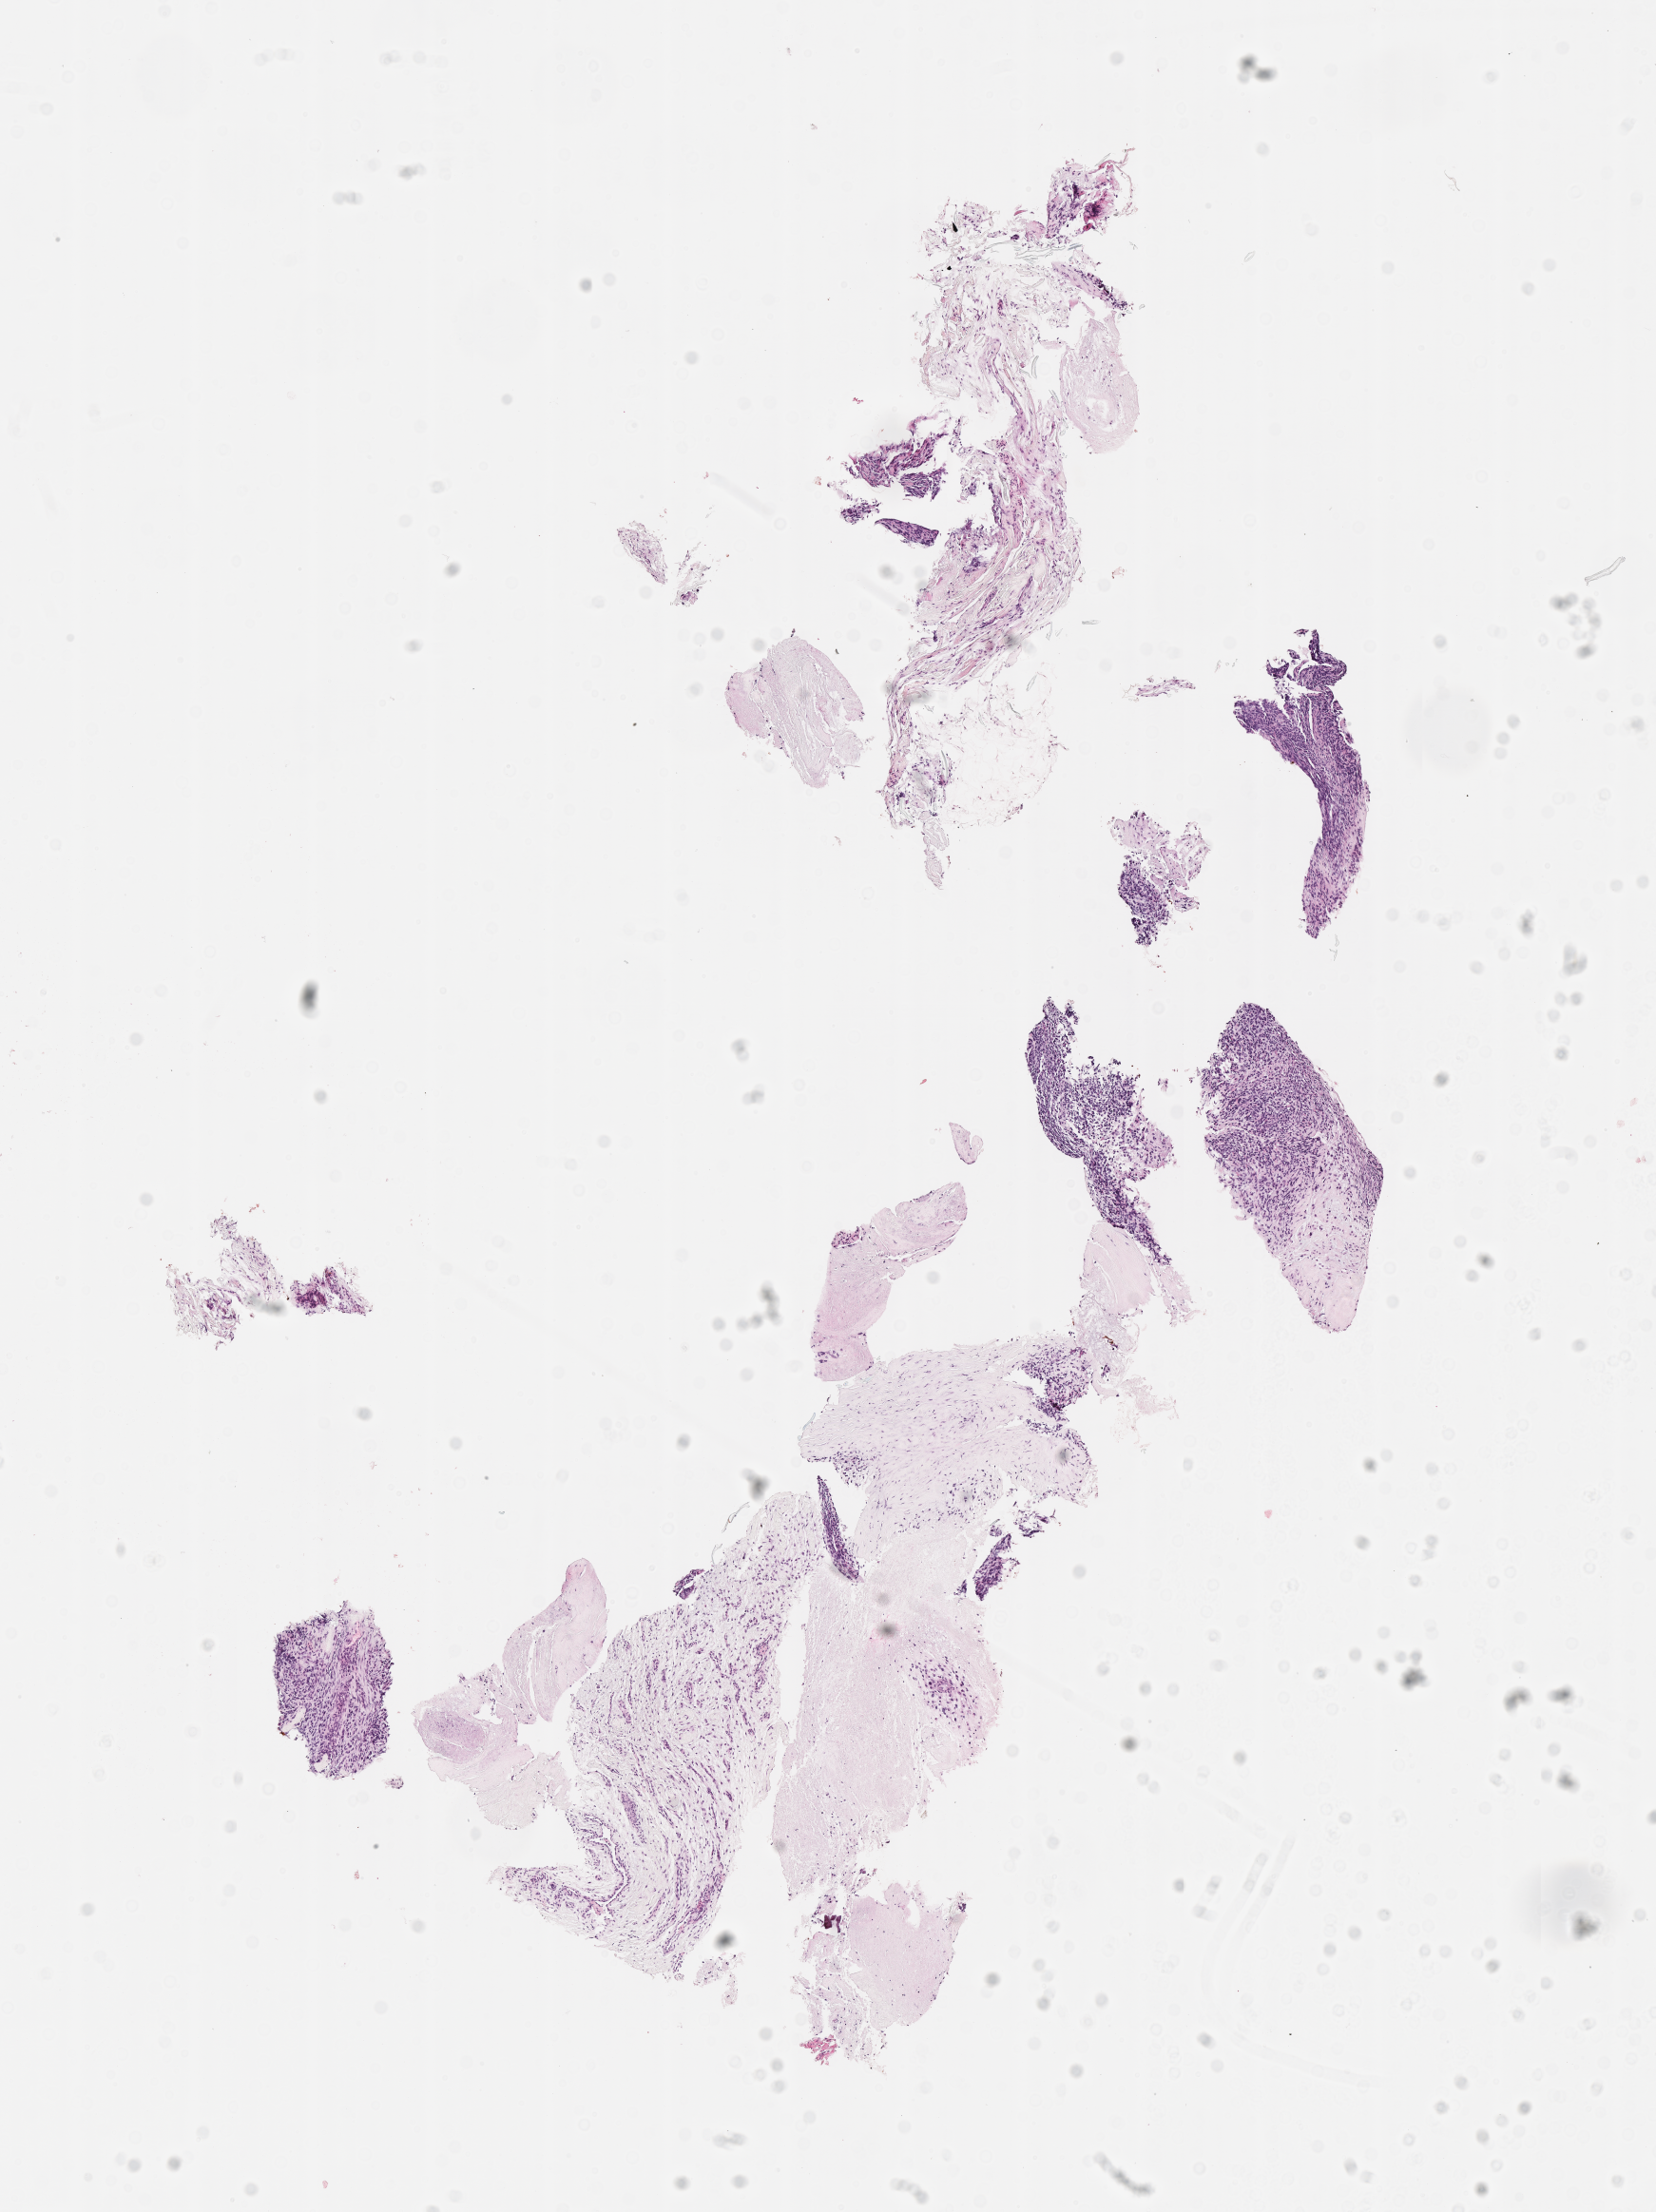
Whole-slide image, hematoxylin and eosin (H&E) stain of tumor tissue — whole scanned area (about 7.0 x 9.4 mm) shown as a low-resolution overview; formalin-fixed, paraffin-embedded (FFPE) tissue; sample anatomic site: soft tissue, calf-right. Female patient, age at diagnosis 2.6 years.
Diagnosis: rhabdomyosarcoma; histological classification: embryonal rhabdomyosarcoma.